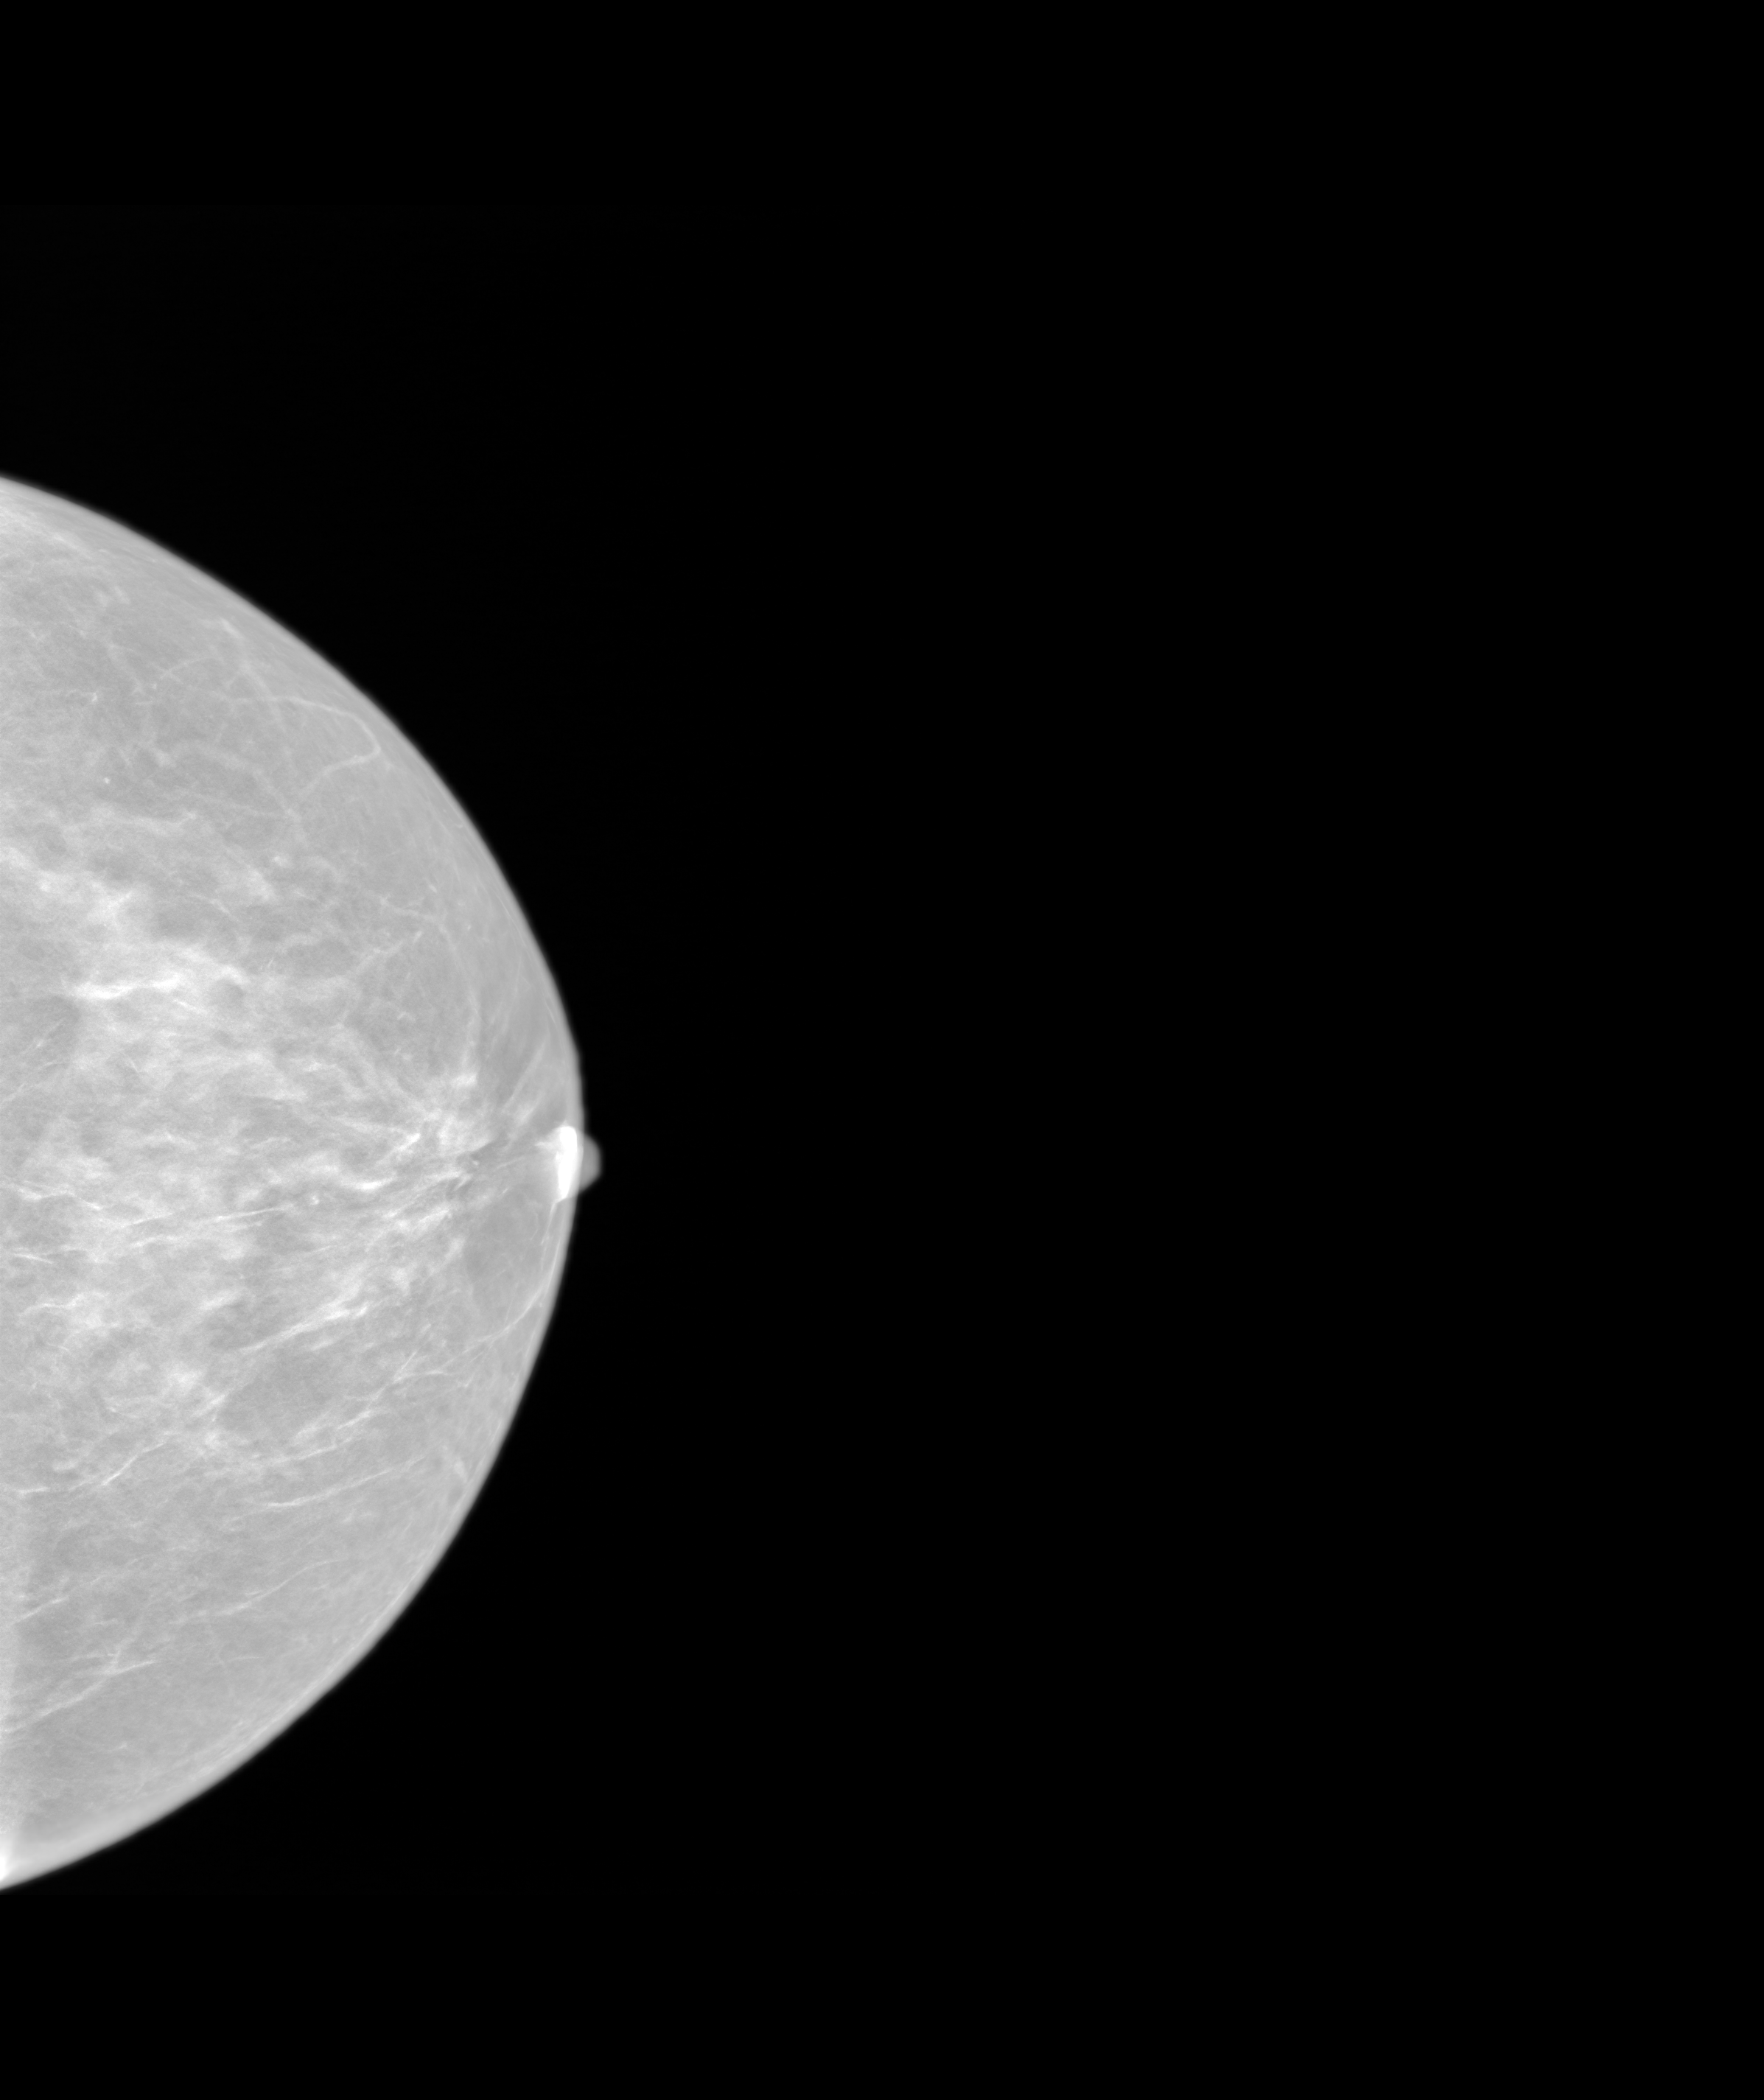
Annual screening mammography examination; system: SenoIris_1SP1.1(421). Patient: female, 49 years.
Image type: synthesized 2-D view from tomosynthesis. Breast: left. Projection: craniocaudal (CC) view.